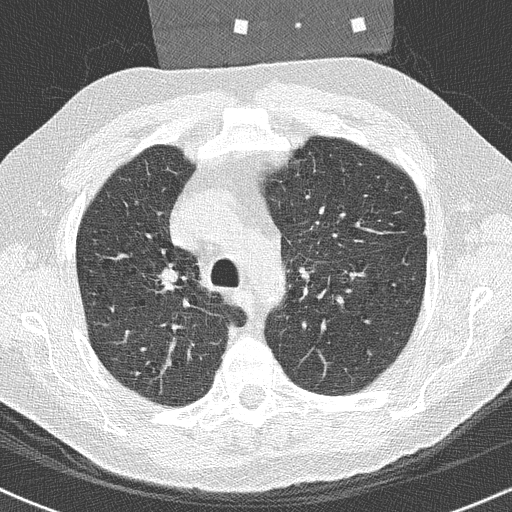
Axial slice from a low-dose chest CT screening exam; baseline annual screen; lung window (W 1500 / L -600 HU); slice 81 of 250 in the series. Male participant, aged 59 years at enrolment. Former smoker at enrolment.
Expert-annotated lung lesion, bounding box (x1, y1, x2, y2) in pixels: (147, 258, 184, 296). No non-calcified nodule or mass ≥4 mm was recorded by the screening reader at this exam. Participant outcome: lung cancer diagnosed 360 days after this screen — squamous cell carcinoma, NOS, right upper lobe, poorly differentiated (G3), stage IIA (AJCC 6th edition), 20 mm at pathology.